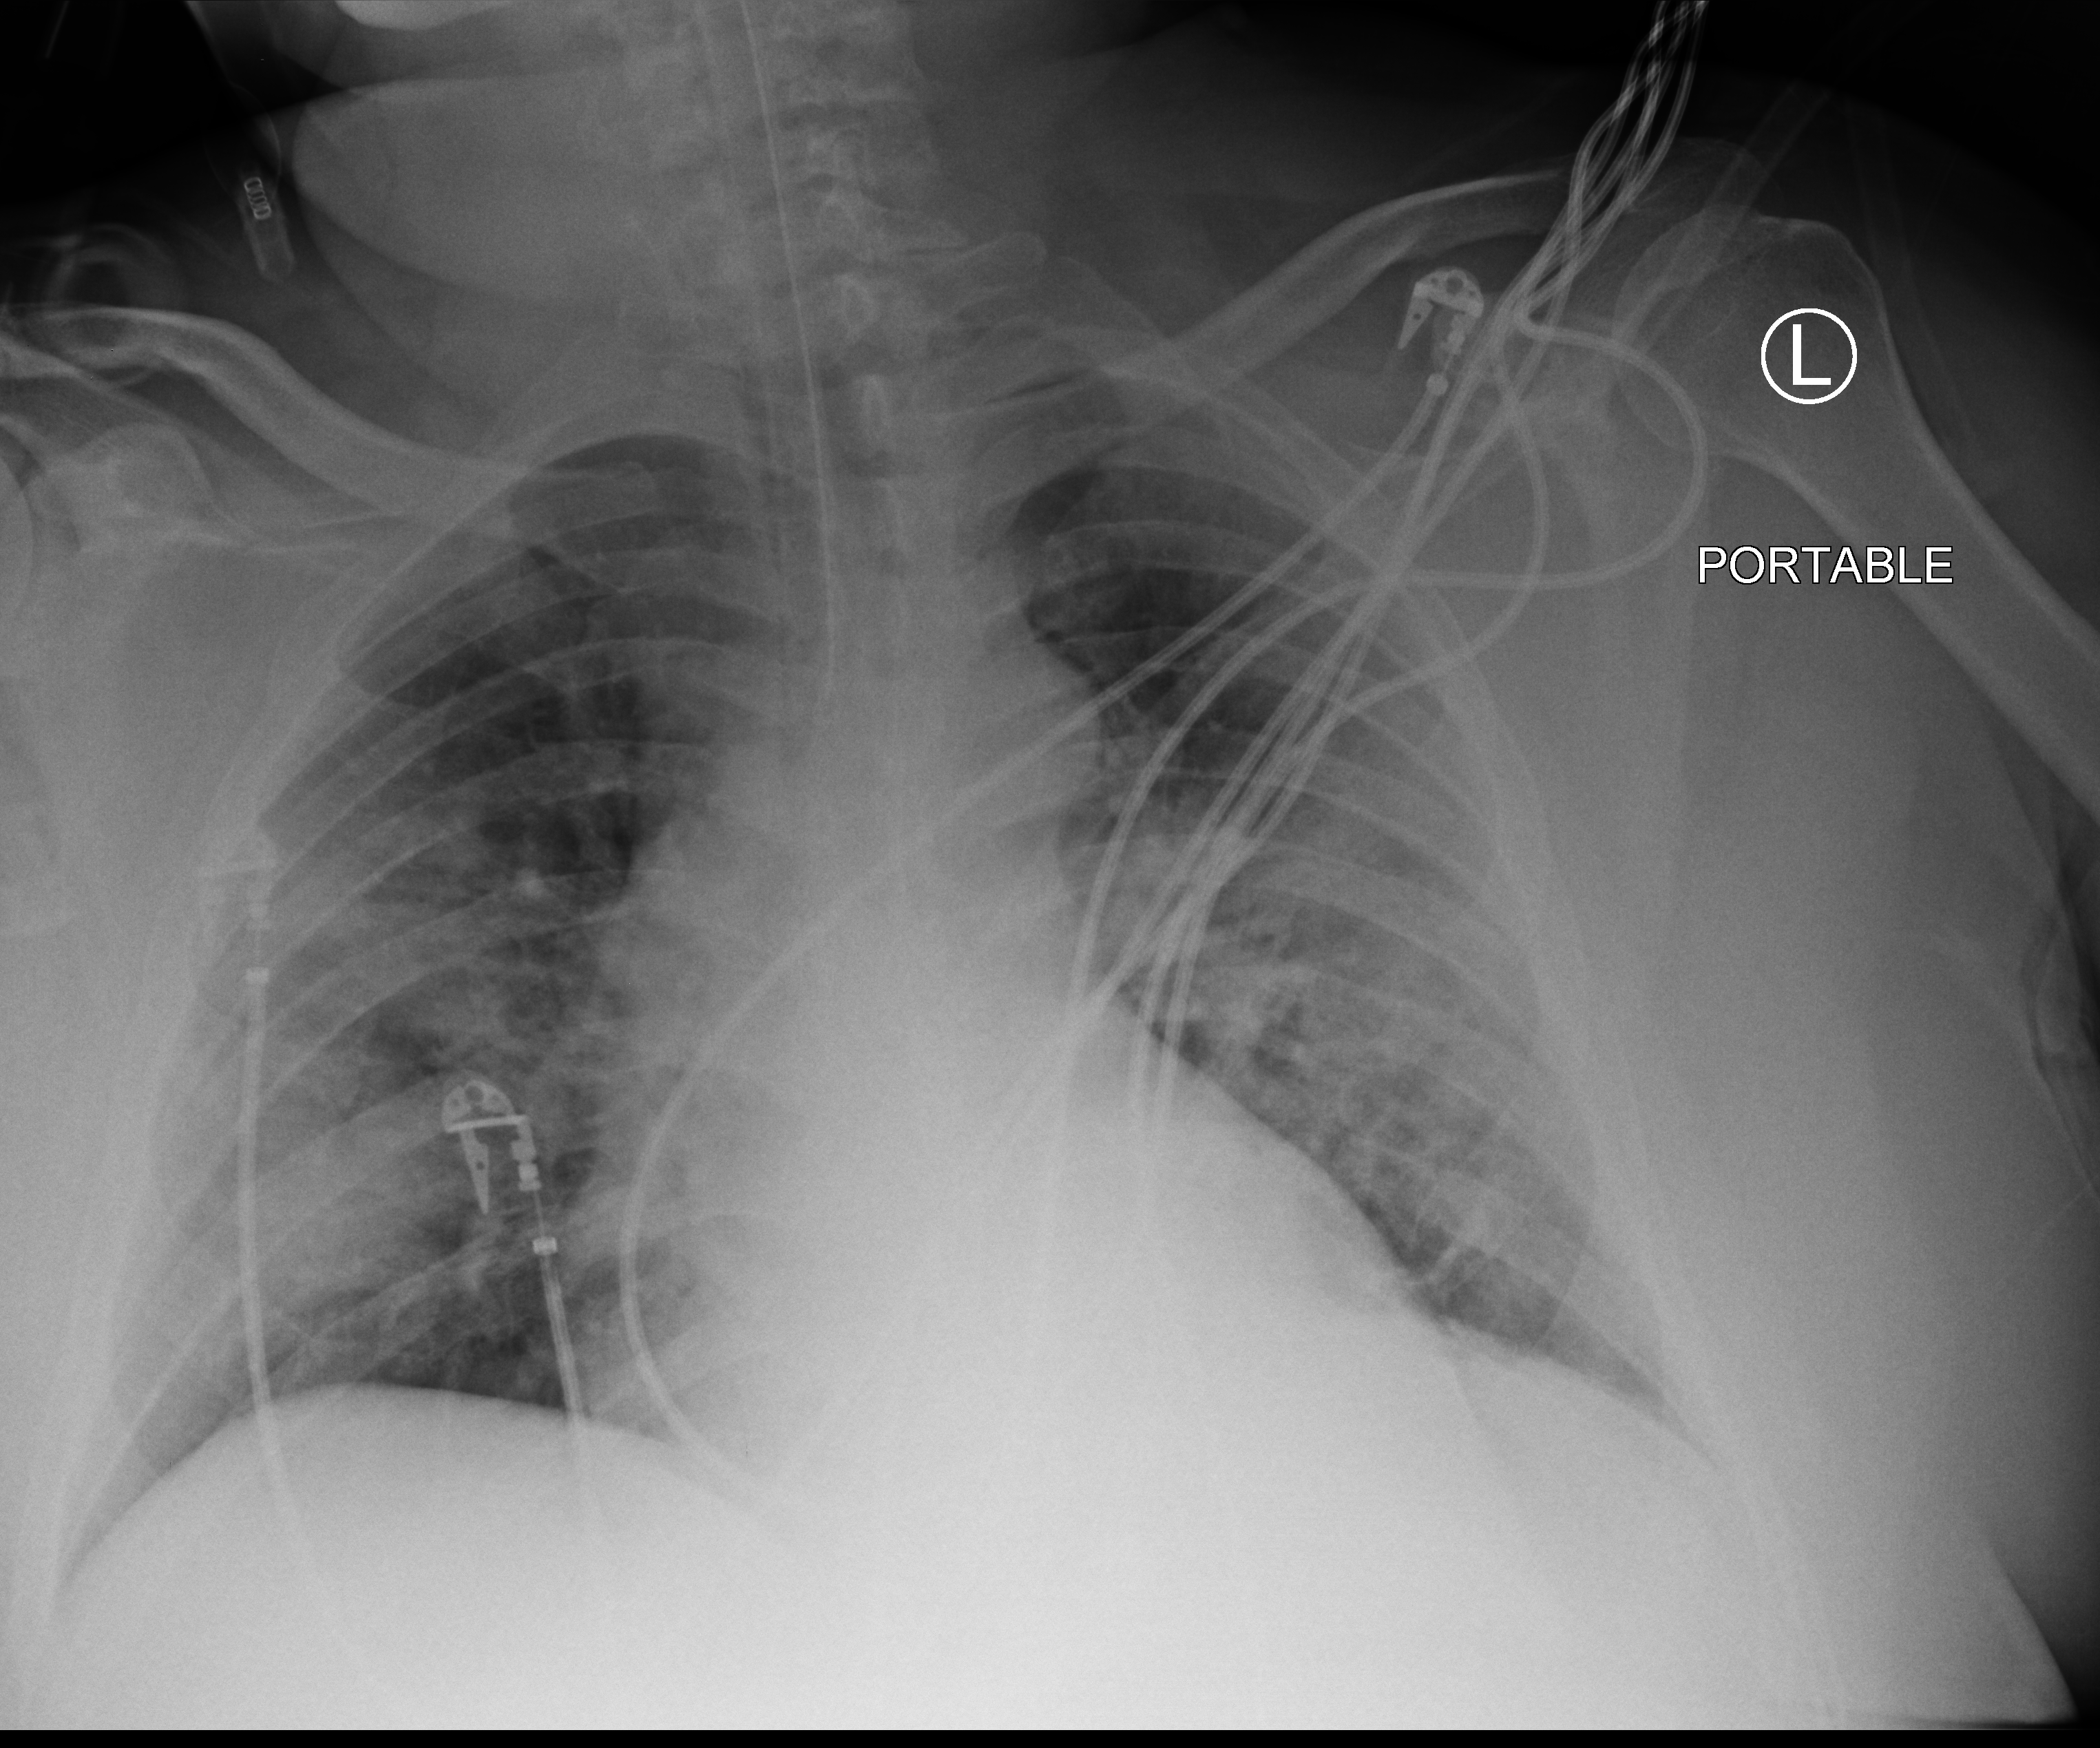
Chest X-ray (portable); anteroposterior (AP) projection. Male patient hospitalised with COVID-19, age 60–74 years.
From the hospital-stay record, not from the radiograph (when in the stay this image was taken is not recorded):
- chronic kidney disease (admission record): no
- admitted to intensive care during this hospital stay: yes
- mechanically ventilated during this hospital stay: yes